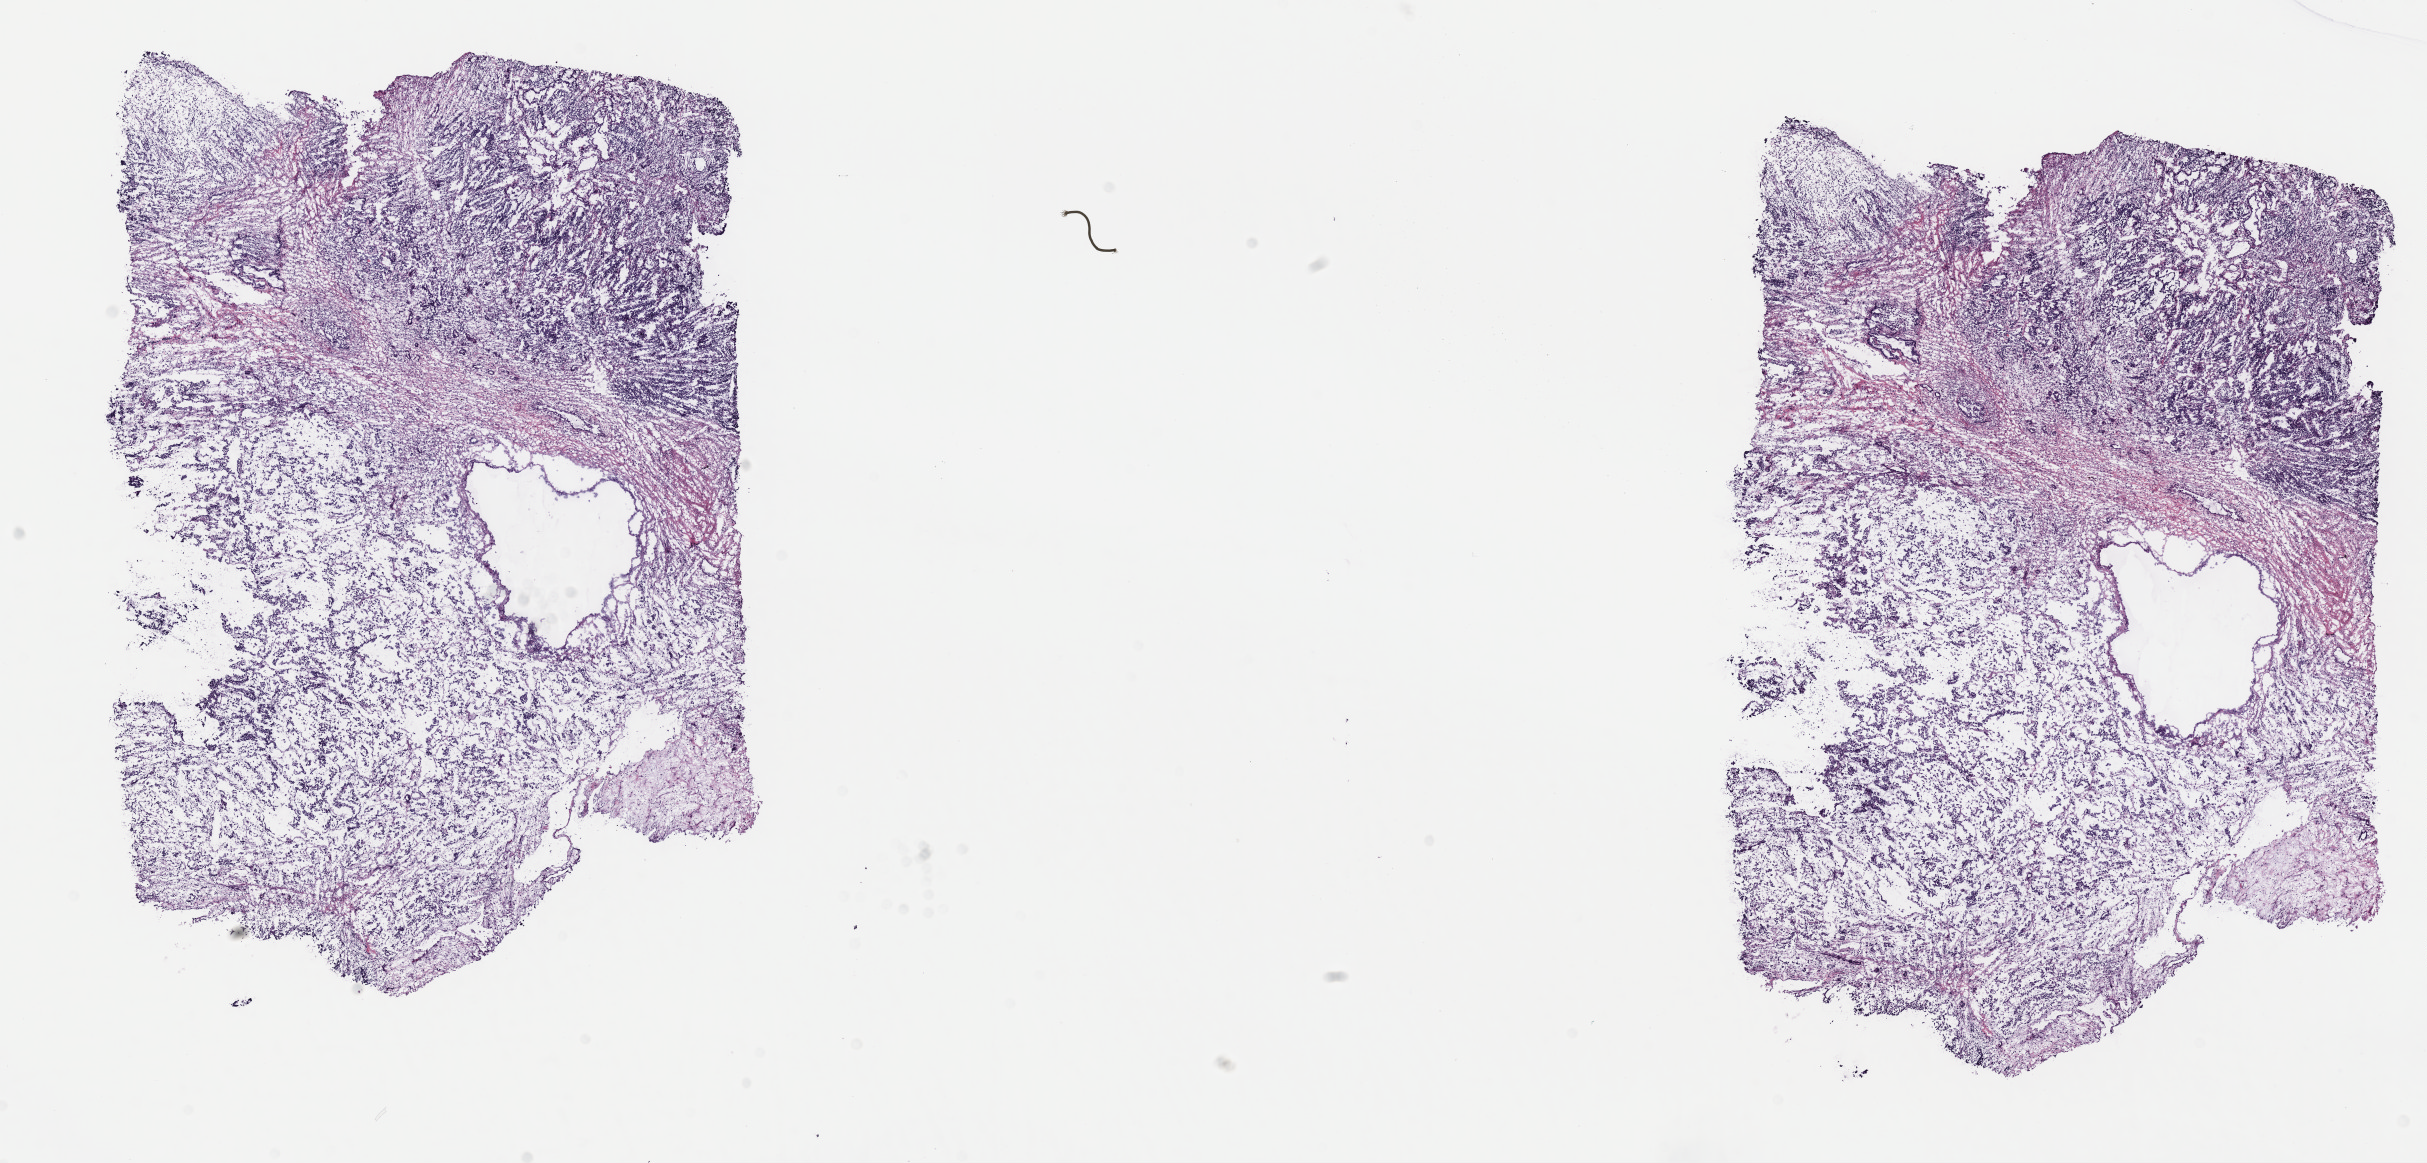
Whole-slide histology image, H&E — a low-resolution overview of the entire scanned area, about 19.6 x 9.4 mm (from a 40x scan); frozen section from the top of the tissue portion; sample: primary tumour, testis. Male patient; age at initial diagnosis 24 years. Composition of this section per pathologist review: tumour cells 70%, tumour nuclei 70%, normal cells 0%, stromal cells 25%, necrosis 5%. Infiltration values recorded for this section: lymphocyte infiltration 70%, monocyte infiltration 10%, neutrophil infiltration 10%.
TNM: T1 NX M0. Laterality: left. Diagnosis: Mixed germ cell tumor. AJCC pathologic stage: IS (6th edition).